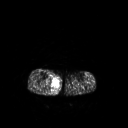
FDG PET of an extremity soft-tissue mass (from a PET/CT study), one axial slice. 128 × 128 image matrix, field of view 500 × 500 mm. Patient: male, 69 years. Case-level facts recorded for this patient, not image findings: histological type: pleiomorphic liposarcoma; grade: high; site of the primary tumour: right calf.
Structures marked on this image (expert contour drawn on MRI and transferred to this co-registered scan by the dataset authors):
- gross tumour volume including surrounding oedema: bounding box (x1, y1, x2, y2) in pixels: (51, 77, 60, 93)
- gross tumour volume (mass): (52, 79, 58, 86)